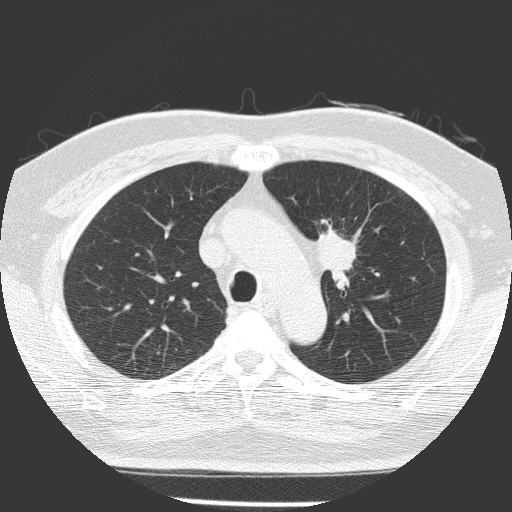
Low-dose screening chest CT, one axial slice; position 111 of 156 along the scan axis; reconstruction kernel FC51; 120 kVp; lung window (W 1500 / L -600 HU); 2 mm slice thickness; 512 × 512 image matrix, field of view 309 × 309 mm.
Outlined on this slice (outlined manually by an expert reader):
- lesion 1 (tumor, upper lobe of left lung): bounding box [x1, y1, x2, y2] px = [316, 224, 356, 287]